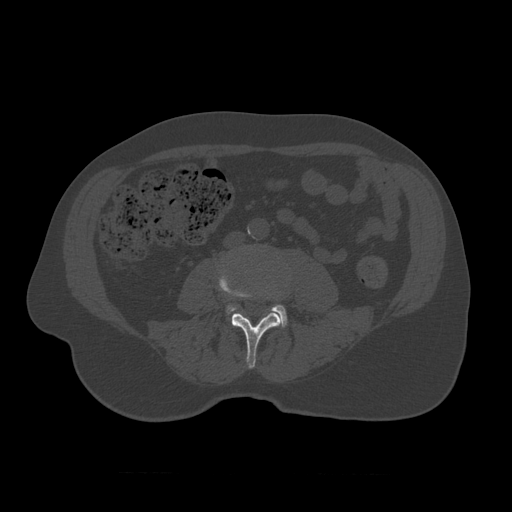
CT including the spine, one axial slice; reconstruction kernel STANDARD; 120 kVp; bone window (W 1800 / L 400 HU); 1.25 mm slice thickness; 512 × 512 image matrix. Patient age 75 years. From the clinical record (not read from this slice): primary cancer: prostate.
Structures marked on this image (semi-automatic segmentation, software-assisted and operator-edited):
- L3 vertebra: bounding box (x1, y1, x2, y2) in pixels: (218, 270, 282, 369)
- L4 vertebra: (227, 286, 288, 328)